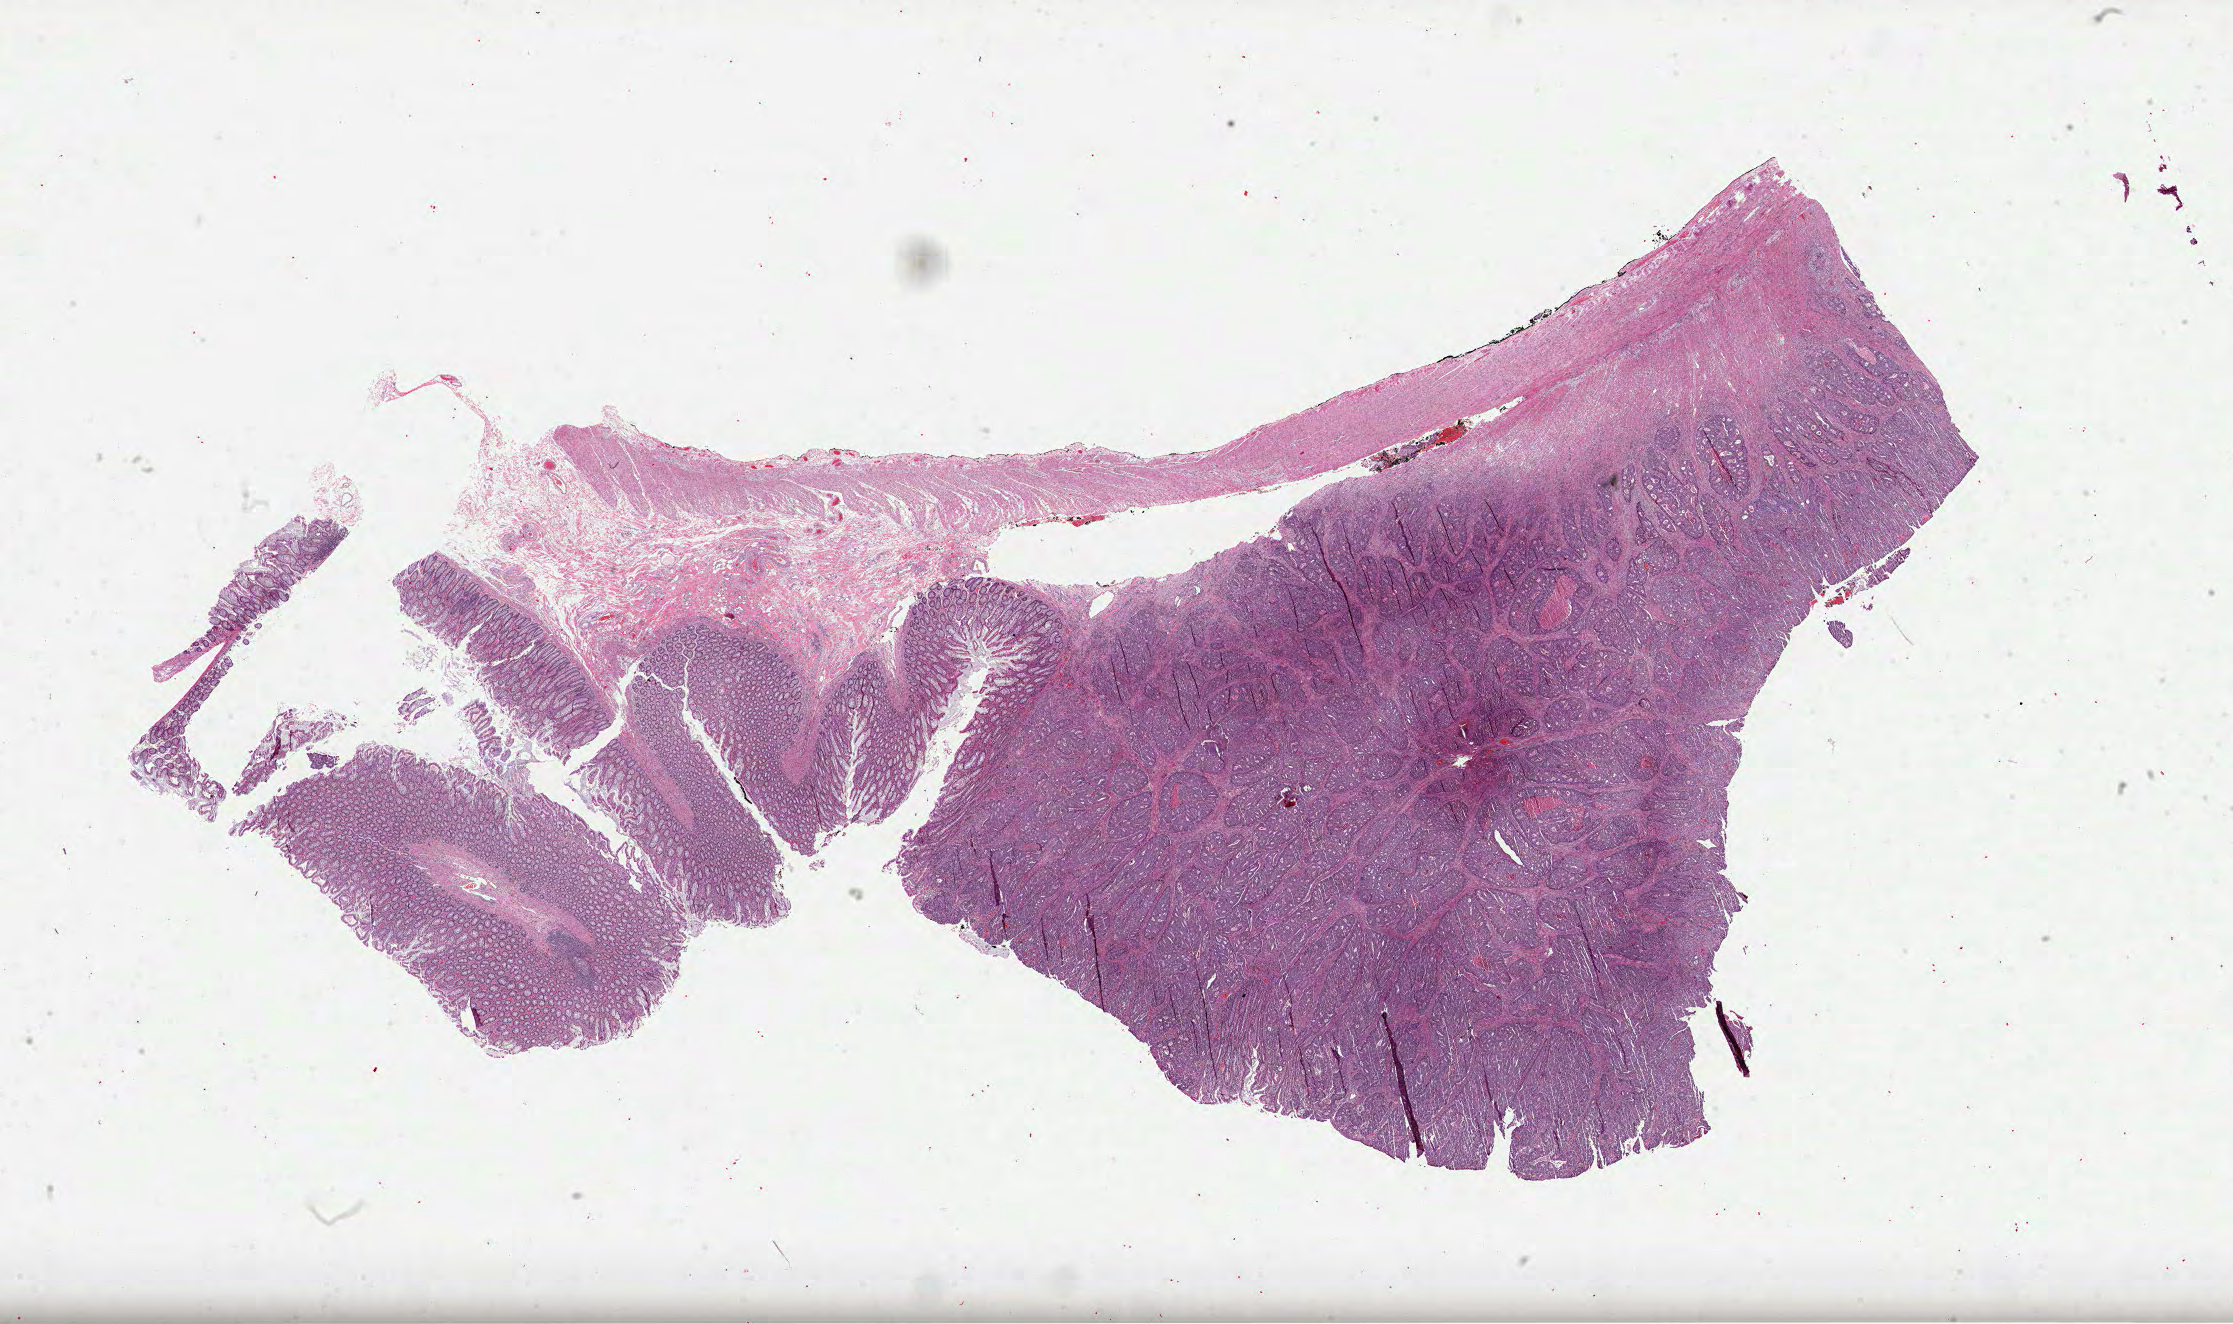
H&E whole-slide image — low-resolution overview of the scanned area, about 36.0 x 21.4 mm (acquisition: 40x scan). Formalin-fixed paraffin-embedded (FFPE) diagnostic section. Primary tumour sample from the colon. Patient: female, age at initial diagnosis 48 years.
Diagnosis: Adenocarcinoma, NOS (ascending colon).